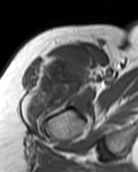
MRI of an extremity soft-tissue mass, one axial slice. Slice 80 of 99 in the series (ordered by position). MR volume resampled by the dataset authors to the PET/CT grid (not the native acquisition matrix). 3.27 mm slice thickness. 138 × 172 image matrix, field of view 135 × 168 mm. Female patient. Case-level facts recorded for this patient, not image findings: histological type: pleiomorphic undifferentiated sarcoma; grade: high; site of the primary tumour: right quadricep.
Outlined on this slice (expert contour drawn on MRI and transferred to this co-registered scan by the dataset authors):
- gross tumour volume including surrounding oedema: bounding box <26,52,93,122> (left, top, right, bottom; pixels)
- gross tumour volume (mass): <39,52,93,99>